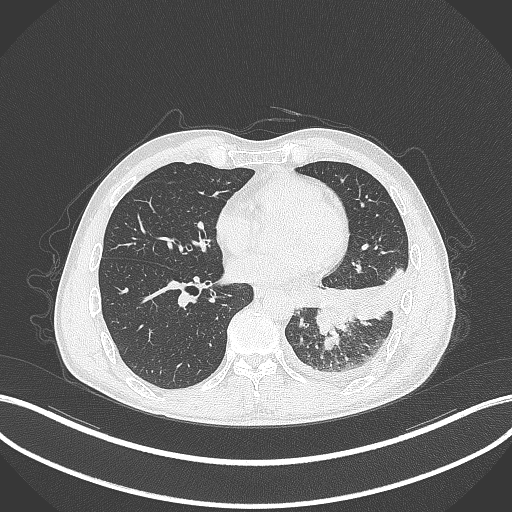
Chest CT, one axial slice; position 124 of 295 along the scan axis; lung window (W 1500 / L -600 HU); 1 mm slice thickness; 512 × 512 image matrix. Male patient, age 47 years. From the clinical record (not read from this slice): clinical TNM (as recorded): T3 N1 M1c.
Structures marked on this image (bounding box drawn by a radiologist):
- lung tumour (recorded histology: small cell carcinoma): bounding box <315,302,355,335> (left, top, right, bottom; pixels)